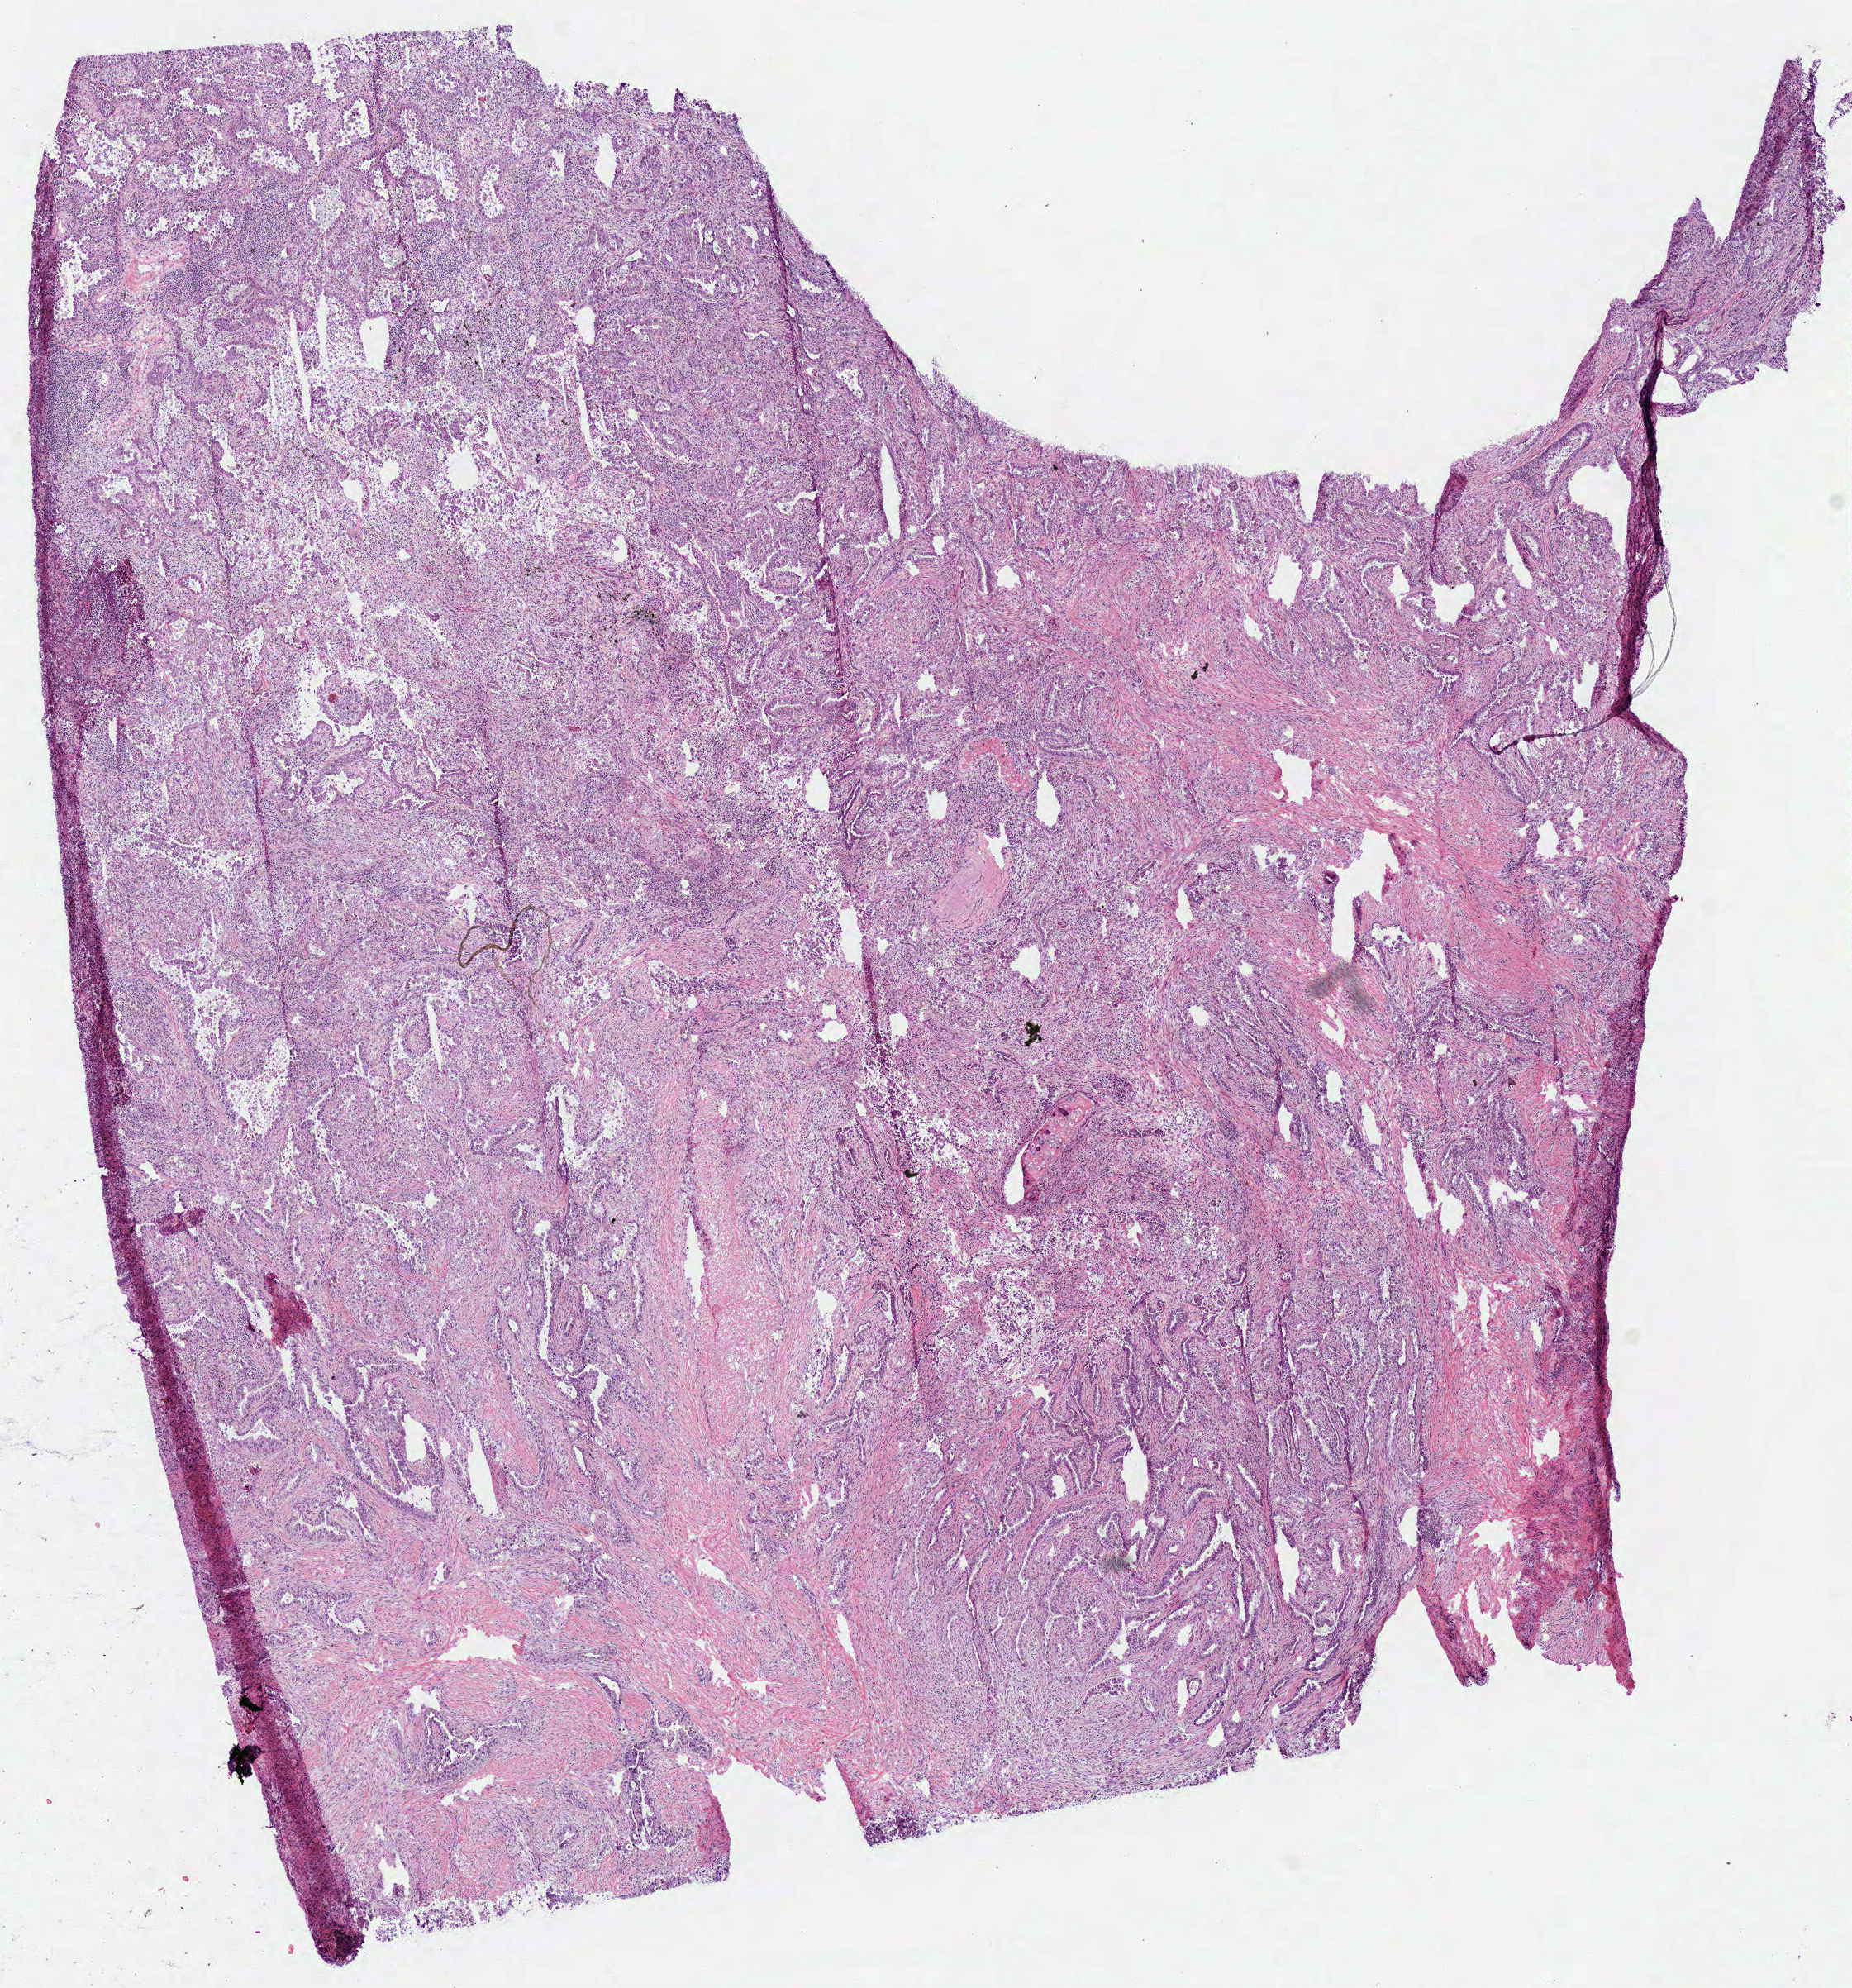
H&E whole-slide image — shown as a low-resolution overview of the whole scanned area (about 8.8 x 9.5 mm), frozen section, primary tumour sample from the lung. Patient: female, age at initial diagnosis 72 years.
Diagnosis: Adenocarcinoma, NOS (upper lobe, lung).